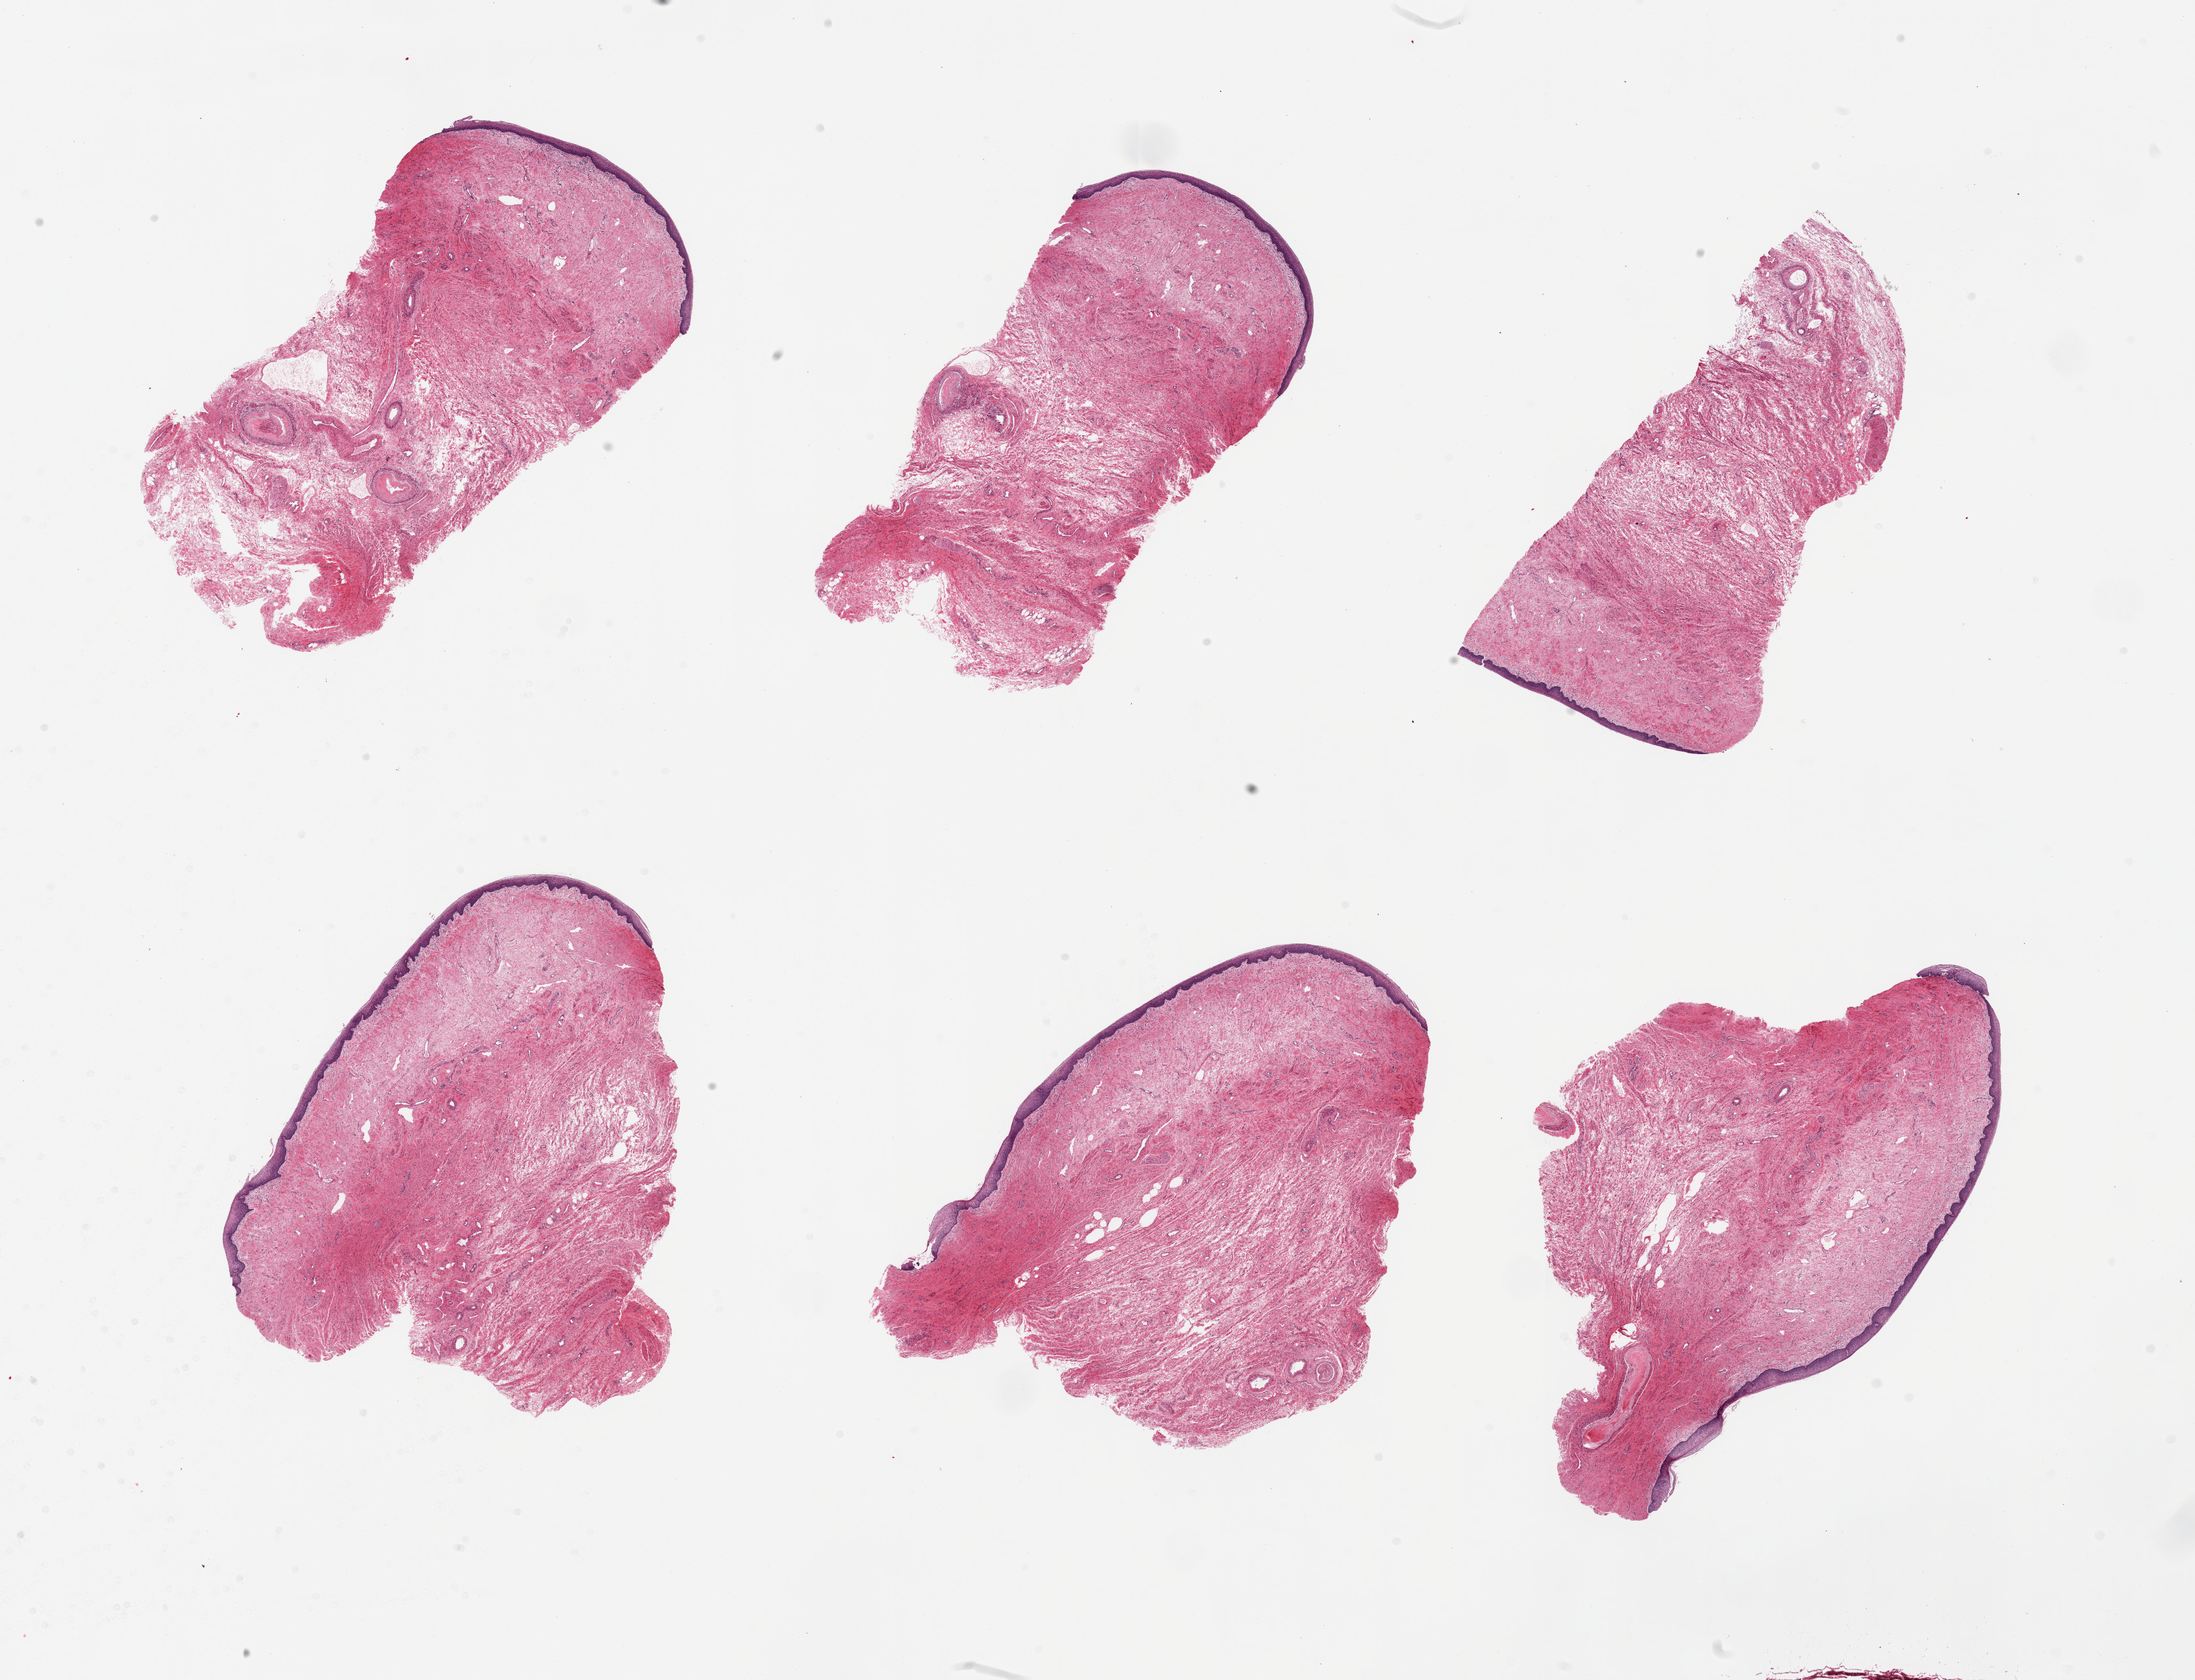
H&E whole-slide image, brightfield — whole scanned area (about 26.6 x 20.3 mm) shown as a low-resolution overview; PAXgene-fixed paraffin-embedded (PFPE) section; section of vagina (target tissue); tissue donor sample.
Review note (as recorded): 6 pieces; atrophic with thin epithelium.